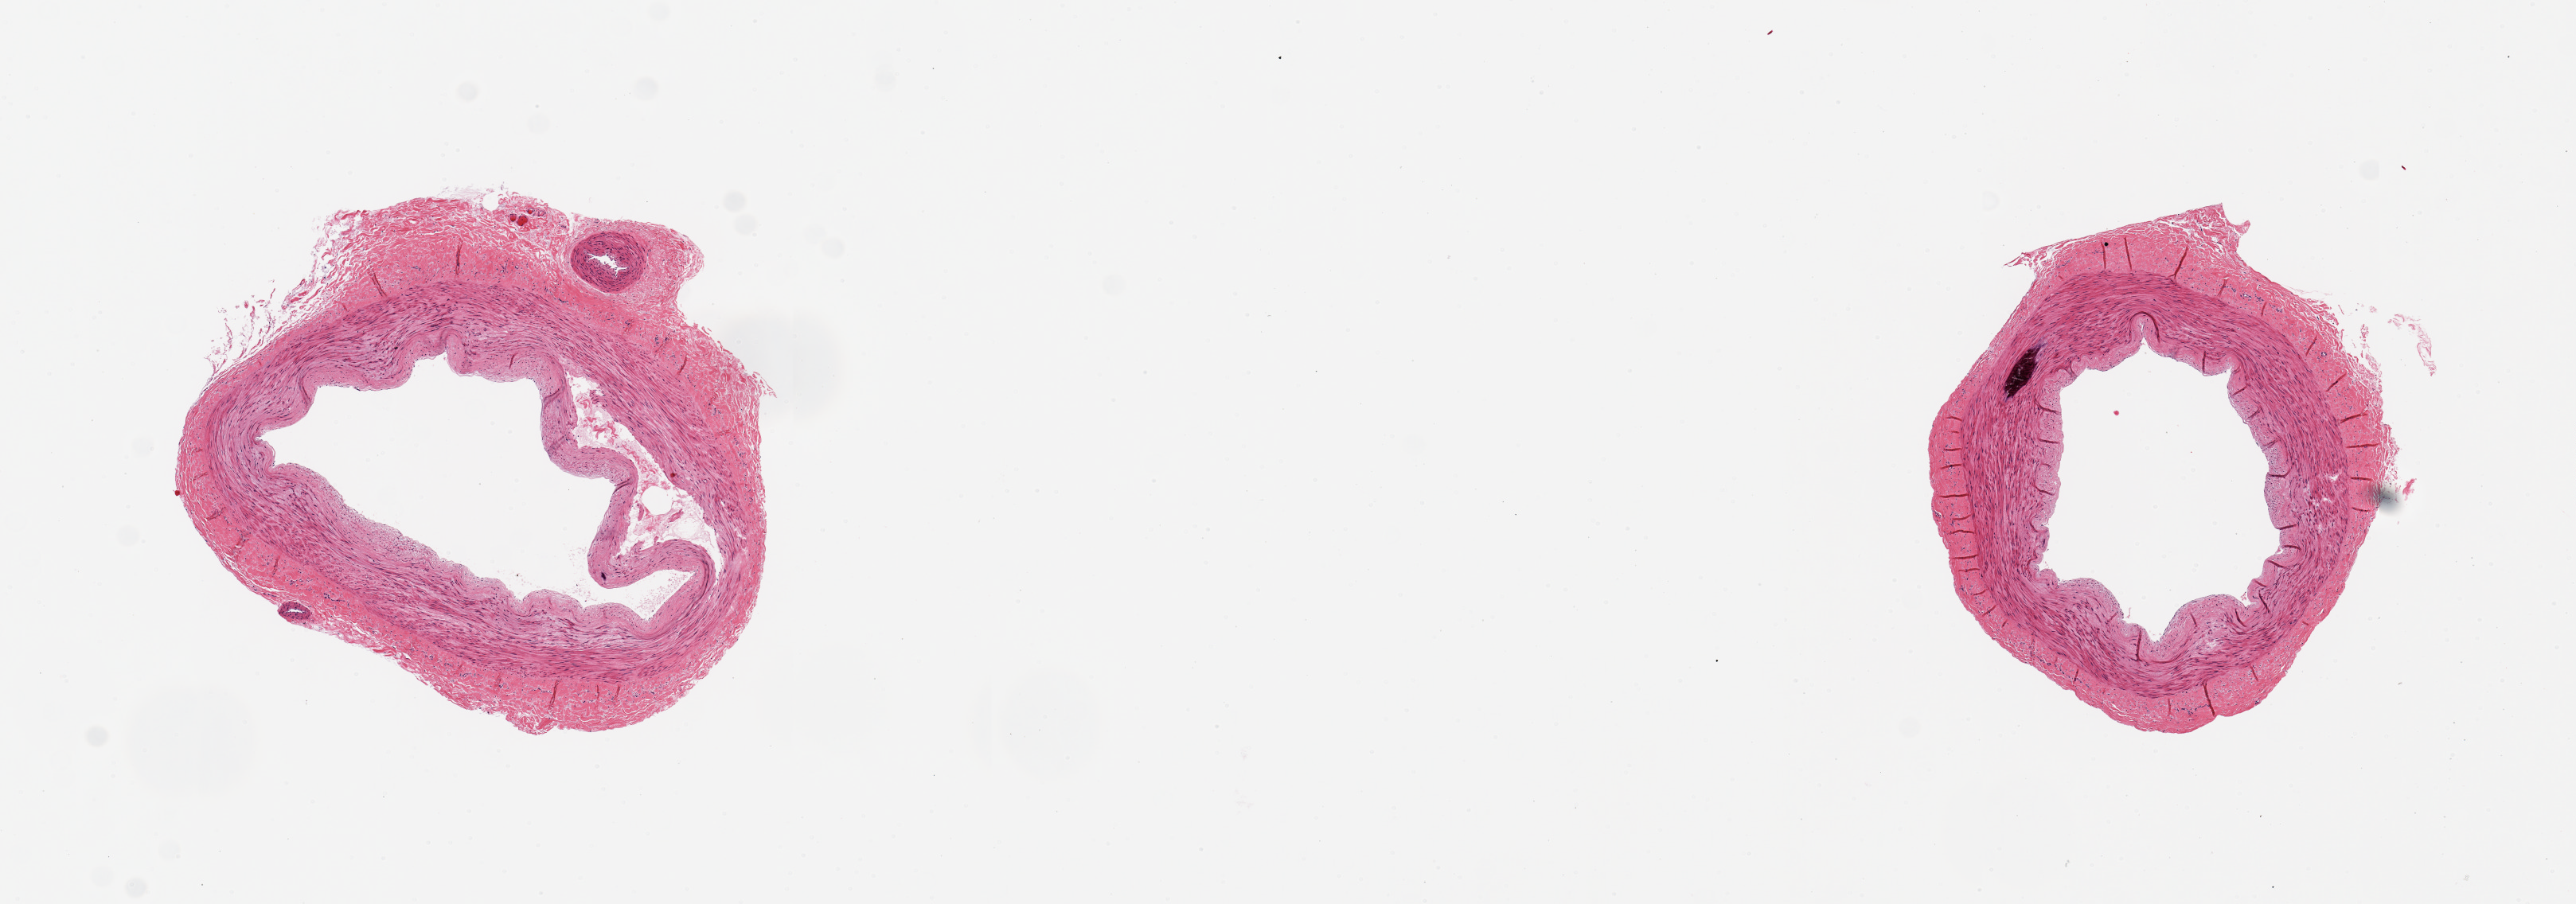
Digitized hematoxylin and eosin (H&E)-stained section, brightfield, shown as a low-resolution overview of the whole scanned area (about 12.8 x 4.5 mm); PAXgene-fixed, paraffin-embedded tissue; target tissue: tibial artery; donor tissue sample. Male donor.
Pathologist's review note for this sample: 2 pieces ~2.5mm d. Clean specimens.